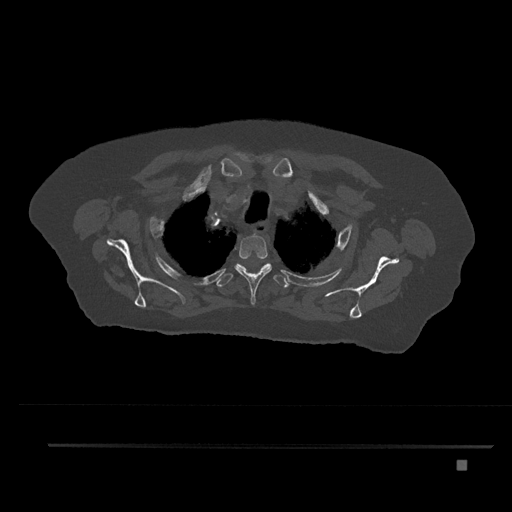
CT including the spine, one axial slice; slice 659 of 797 in the series (ordered by position); bone window (W 1800 / L 400 HU); 0.5 mm slice thickness; 512 × 512 image matrix, field of view 437 × 437 mm. Patient: female, 76 years. Case-level facts recorded for this patient, not image findings: primary cancer: lung.
Structures marked on this image (semi-automatically segmented with operator editing):
- T2 vertebra: box from (x=234, y=235) to (x=272, y=305) px
- T3 vertebra: (x=216, y=263)–(x=288, y=288)